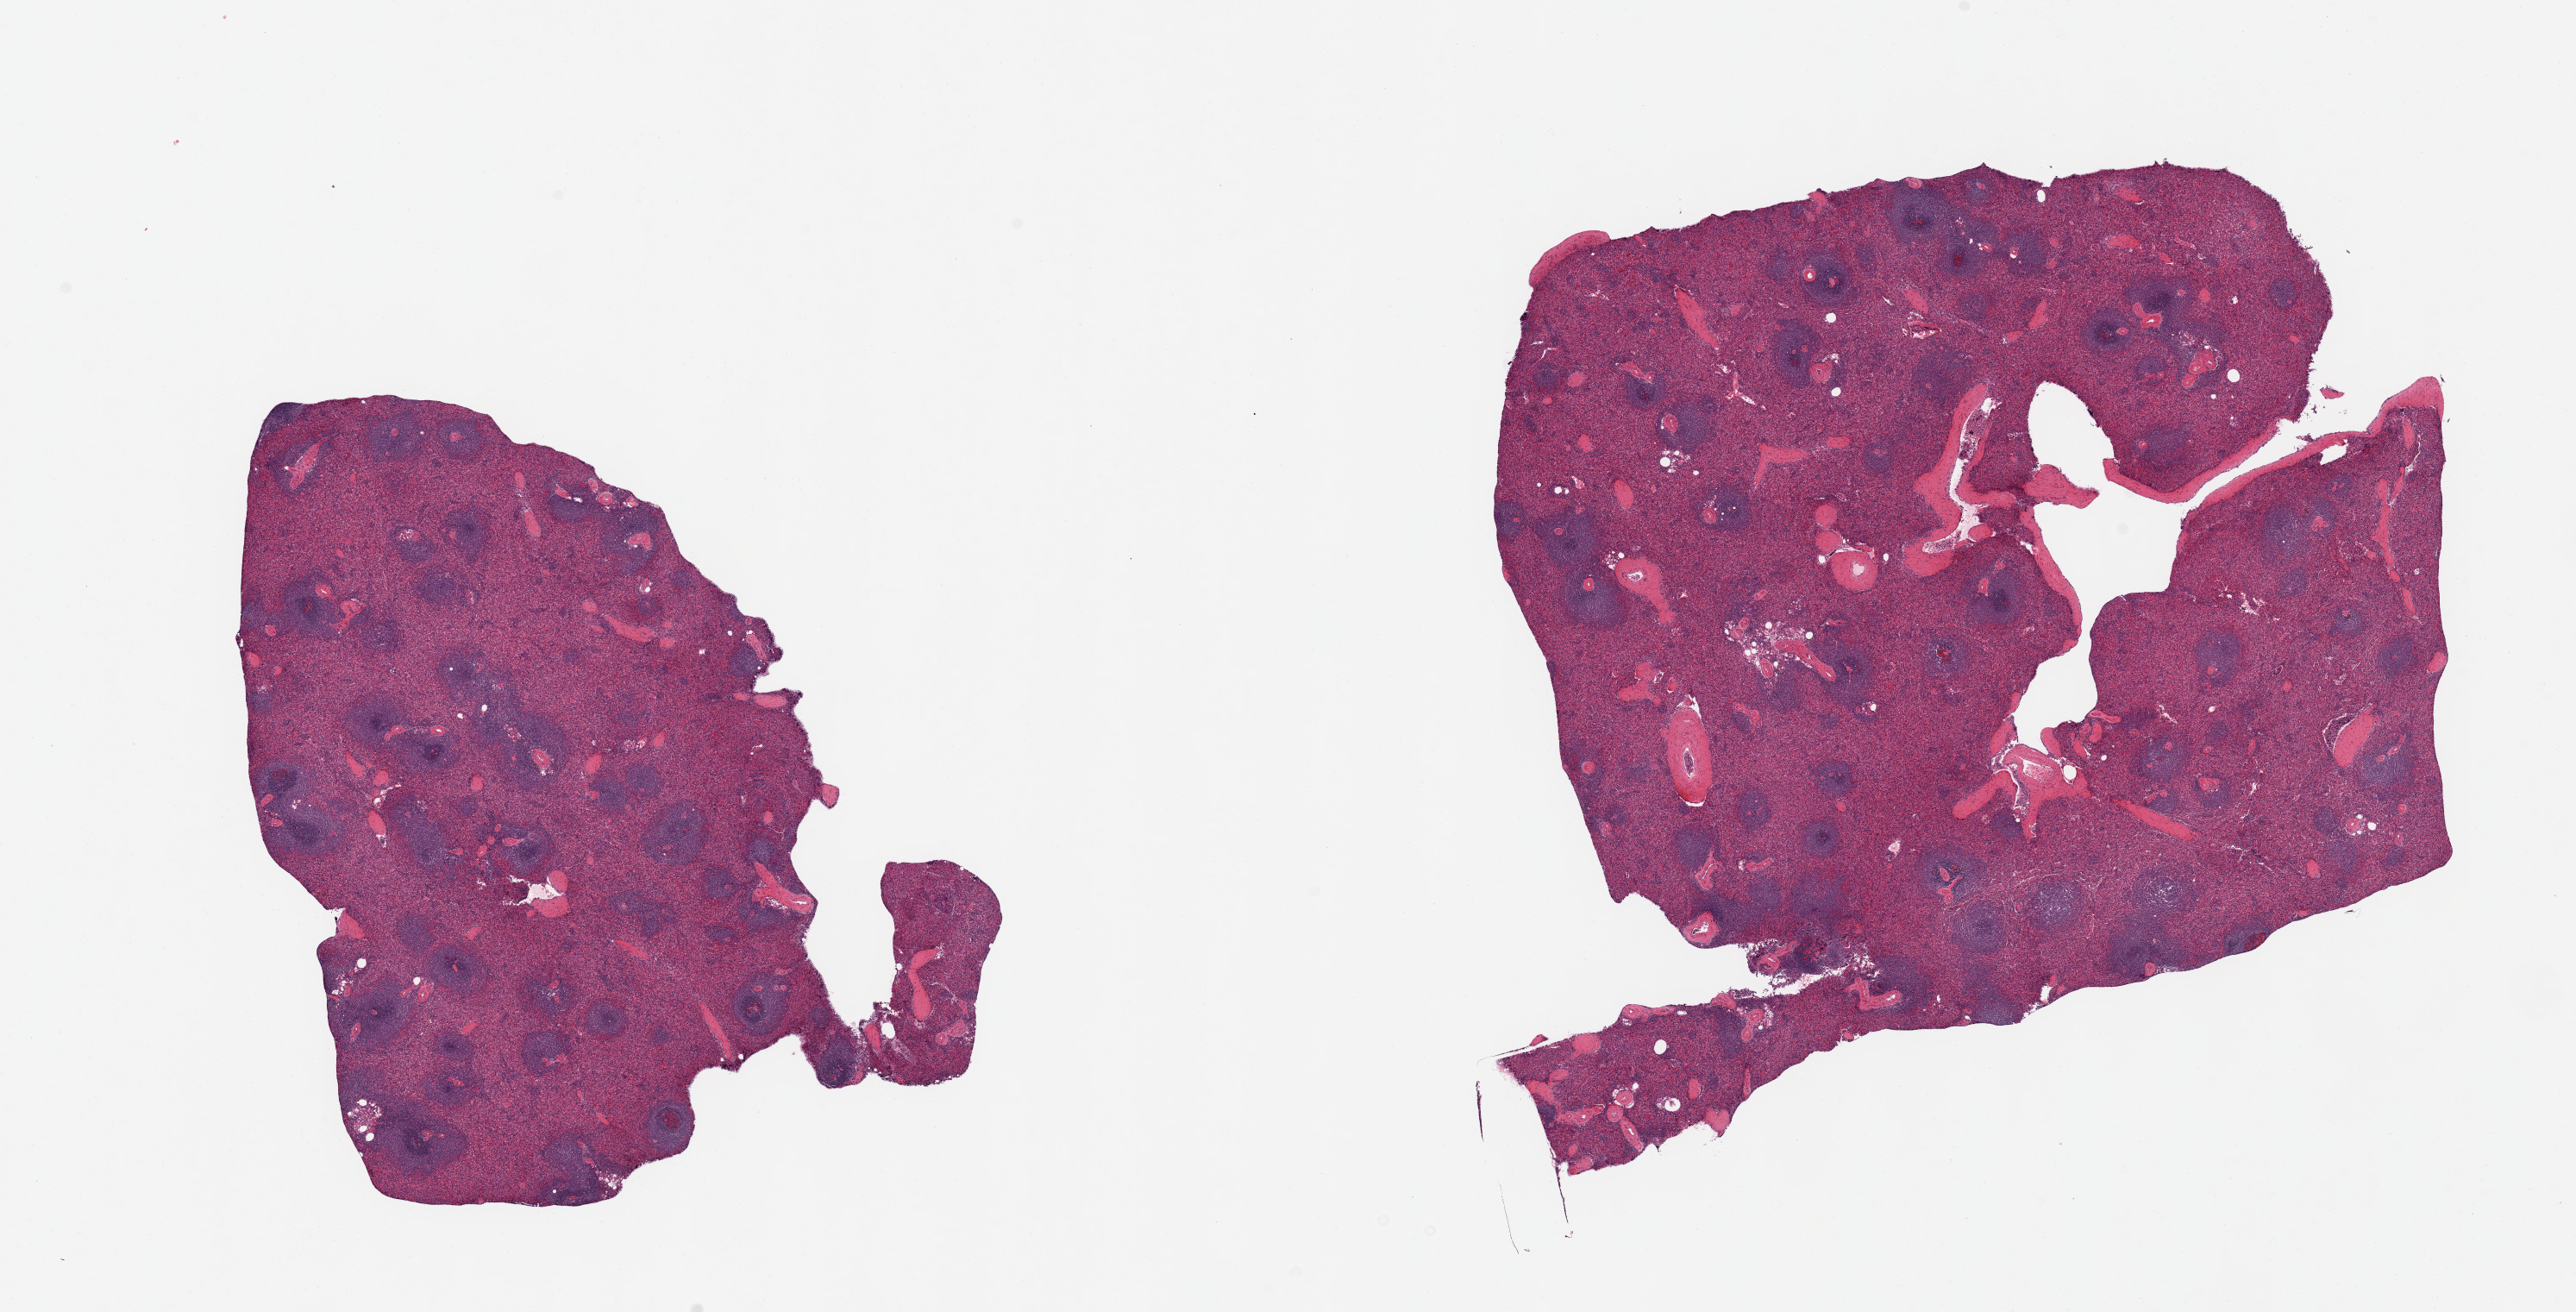
Whole-slide image, H&E stain — a low-resolution overview of the entire scanned area, about 23.6 x 12.0 mm (from a 20x scan); PAXgene-fixed paraffin-embedded (PFPE) section; sampled site (target tissue): spleen; donor tissue sample. Female donor.
- reviewer comment on this tissue sample: 2 pieces, mild congestion